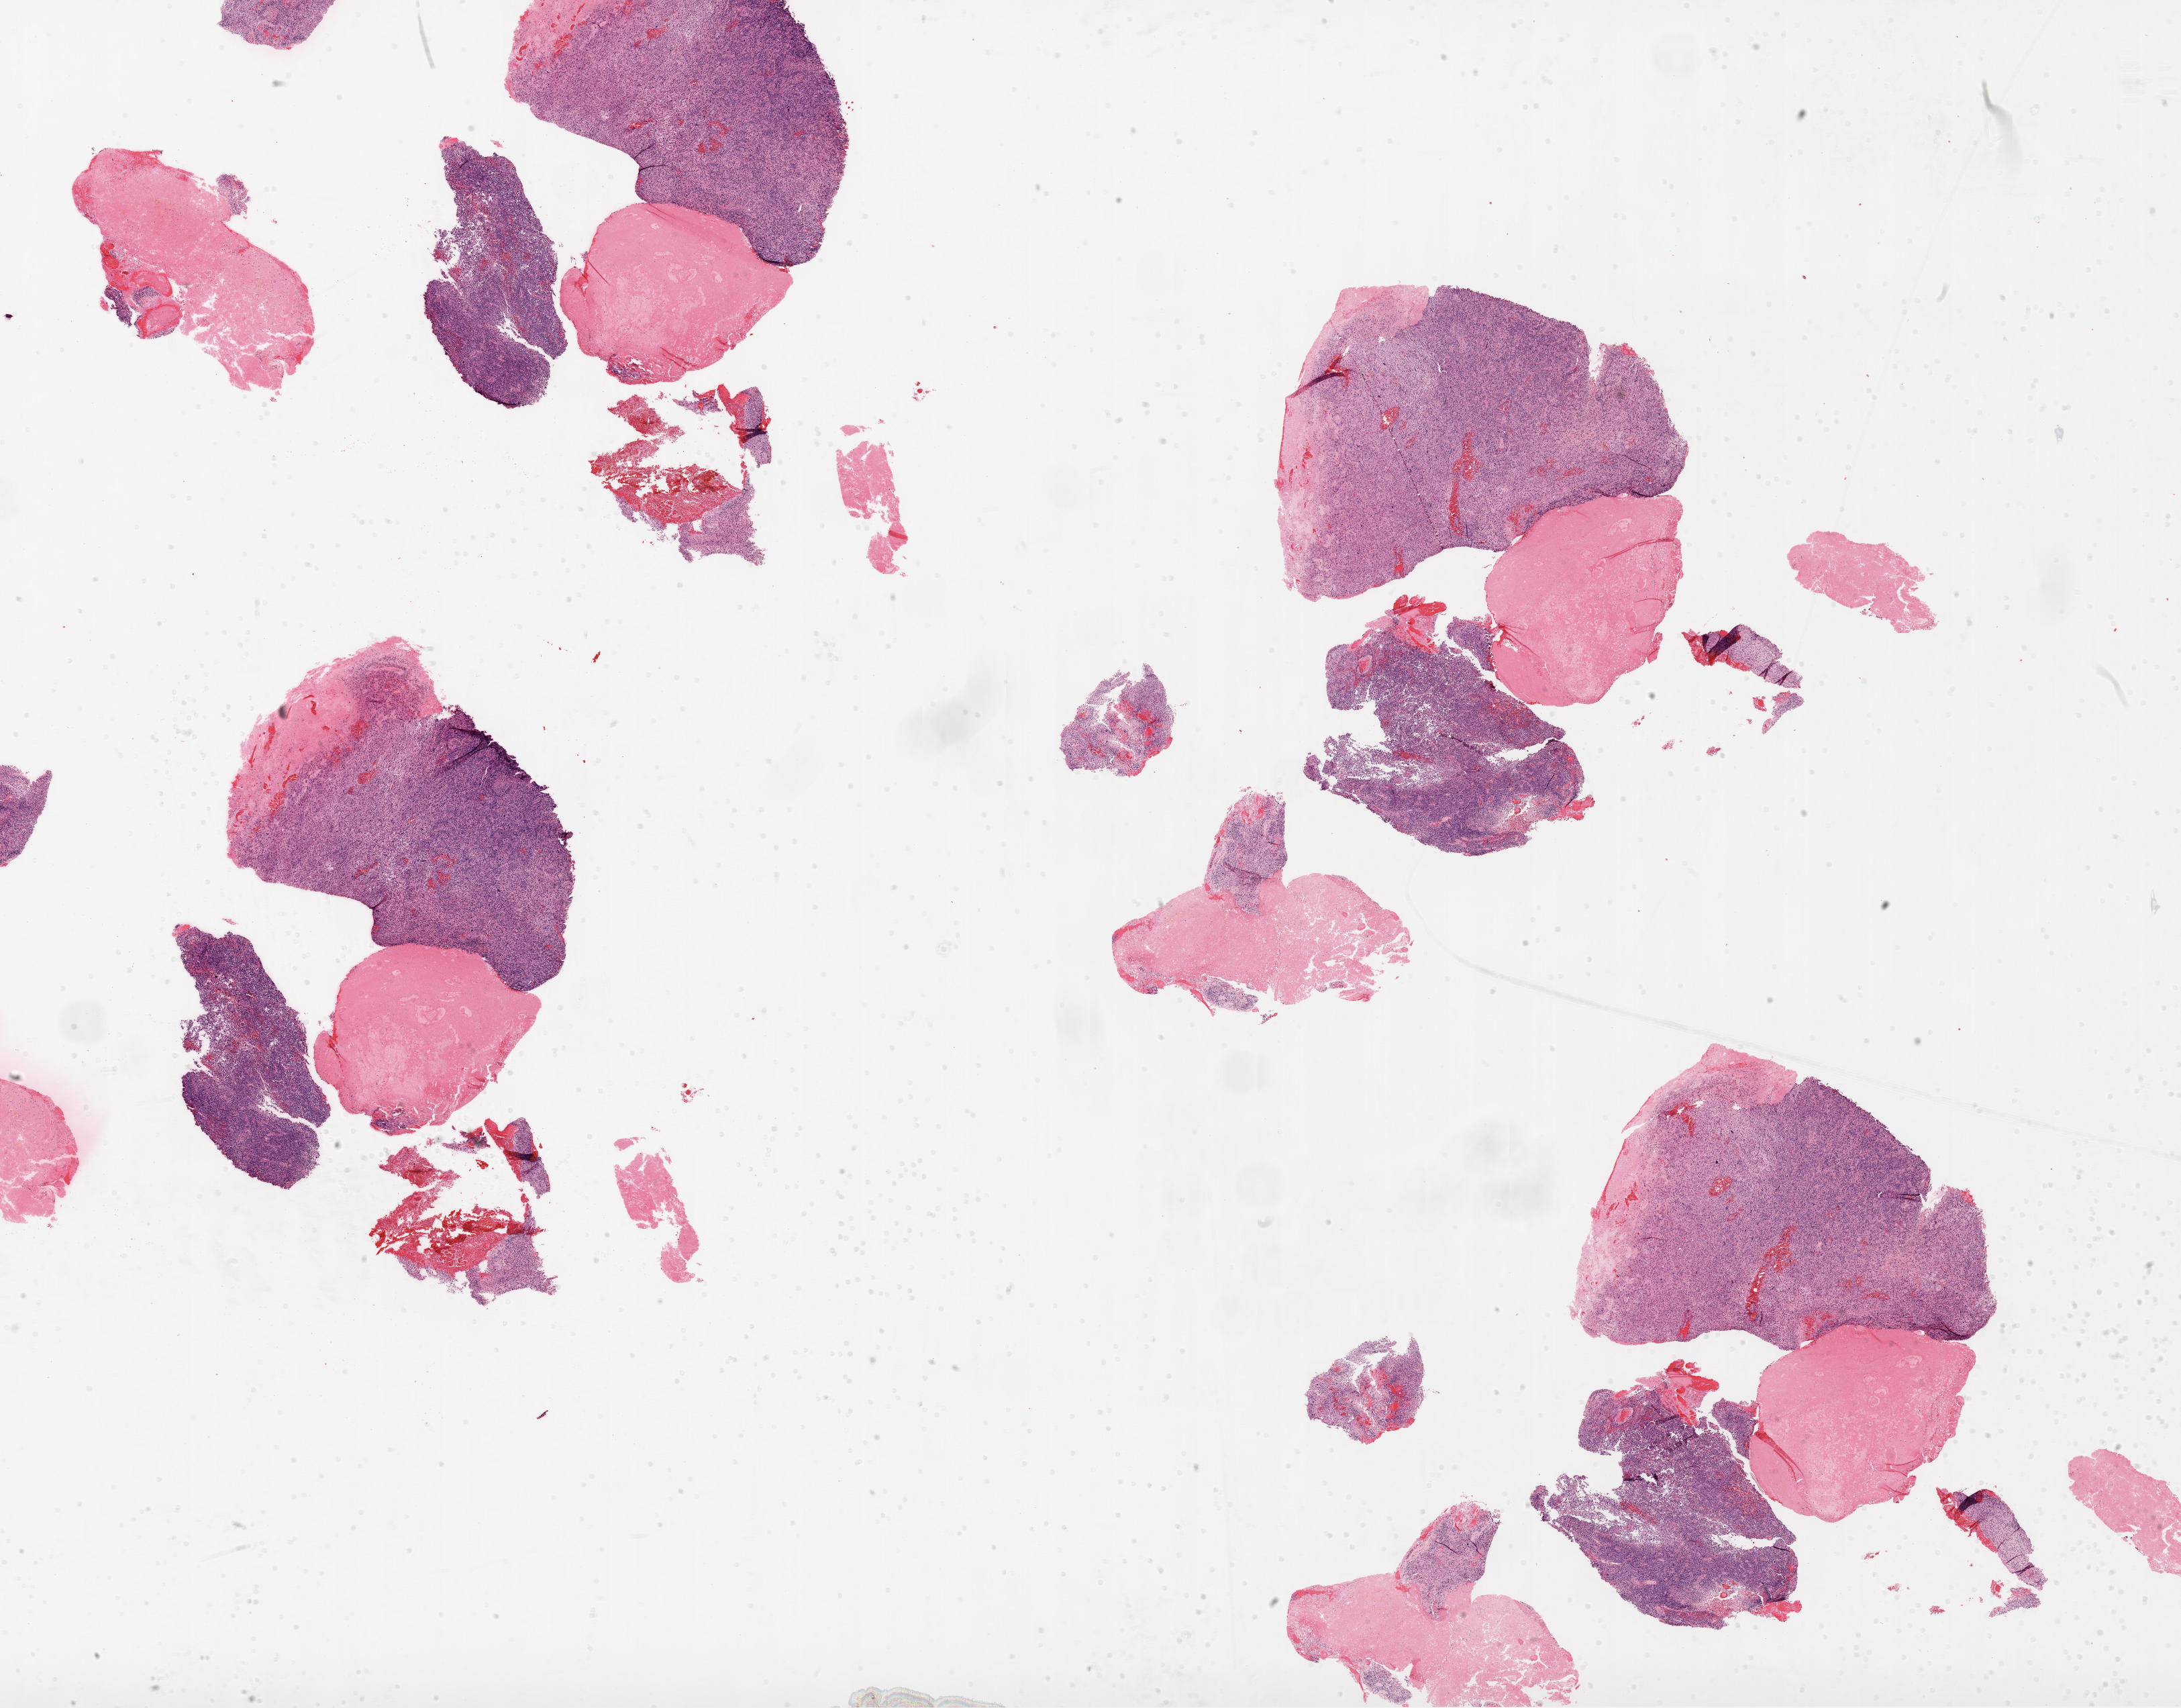
Digitized H&E tissue section (whole slide), a low-resolution overview of the entire scanned area, about 26.1 x 20.4 mm; FFPE section; brain, primary tumour sample. Female, age 36 years at initial diagnosis.
Diagnosis: Glioblastoma.